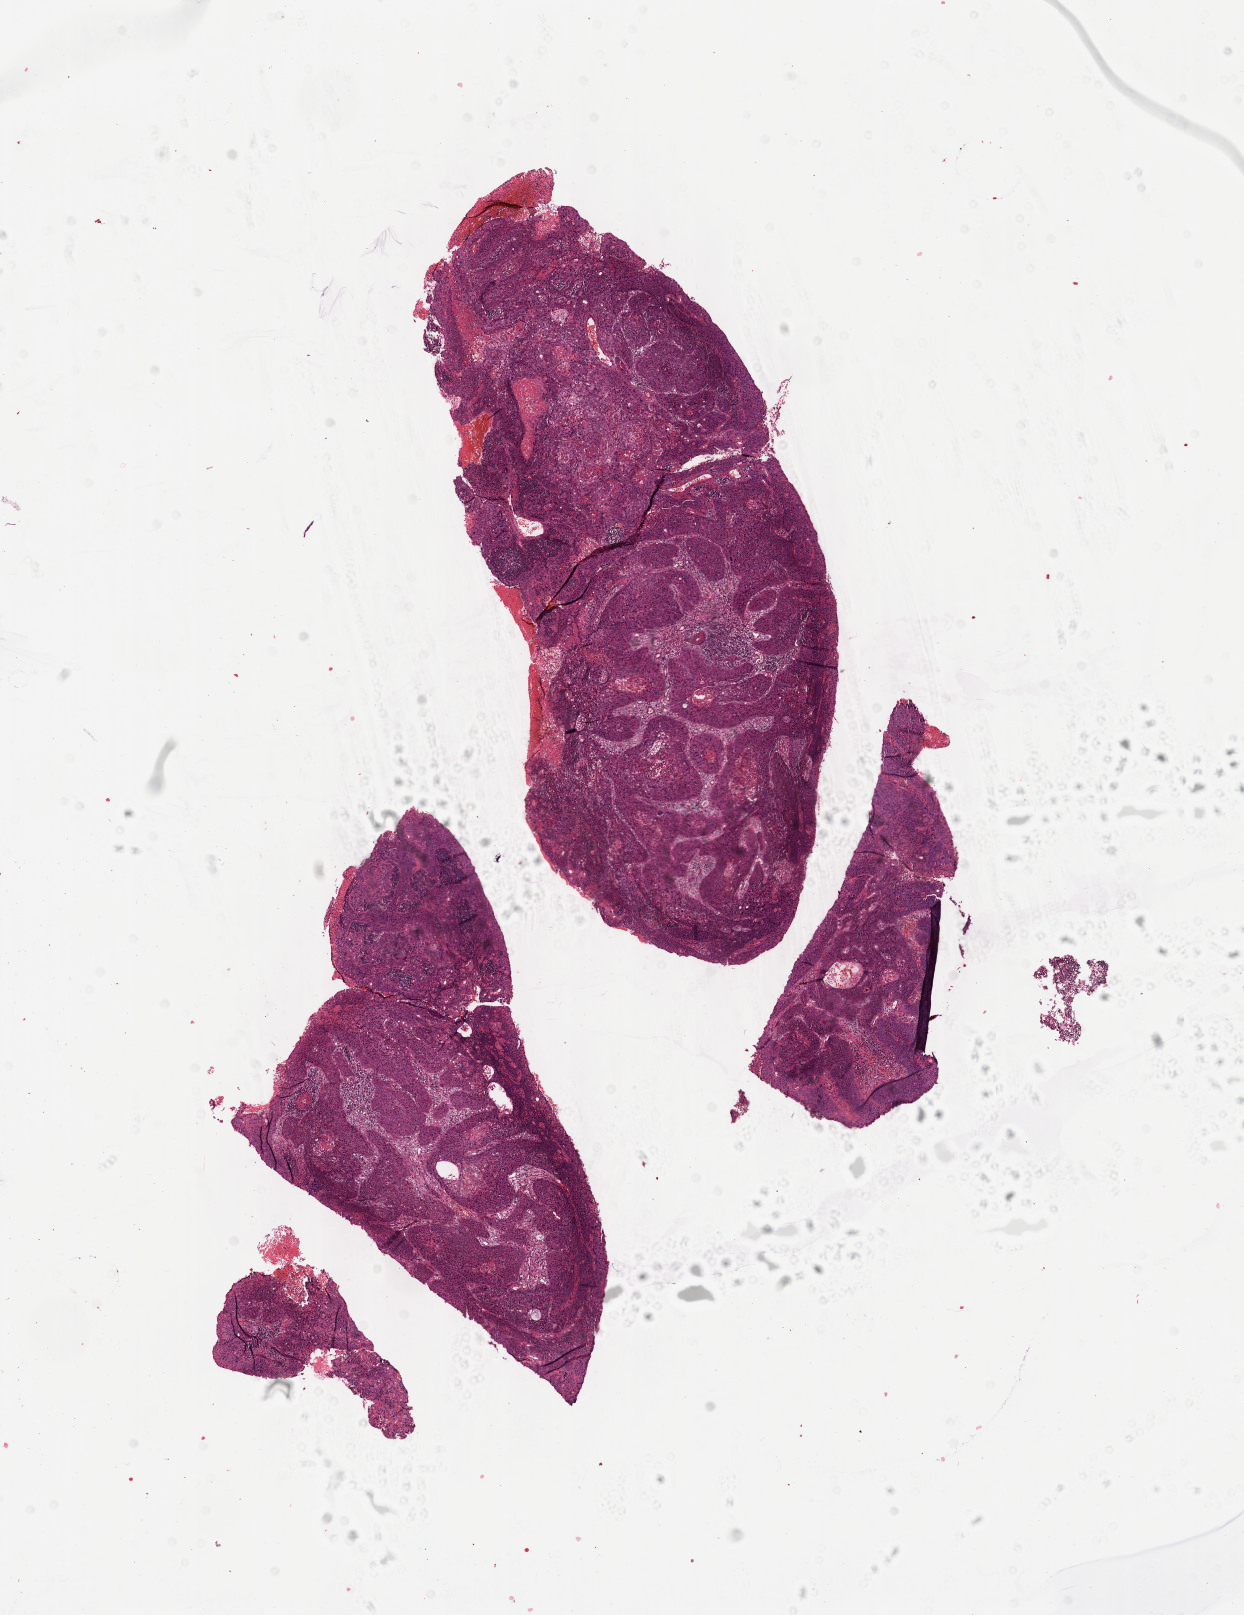
H&E whole-slide image, low-resolution overview of the scanned area, about 10.1 x 13.1 mm (acquisition: 40x scan), formalin-fixed paraffin-embedded (FFPE) diagnostic section, primary tumour sample from the cervix. Female, age 24 years at initial diagnosis. Histologic grade: GX (grade cannot be assessed).
FIGO stage: IIB. Histologic diagnosis: Squamous cell carcinoma, large cell, nonkeratinizing, NOS.